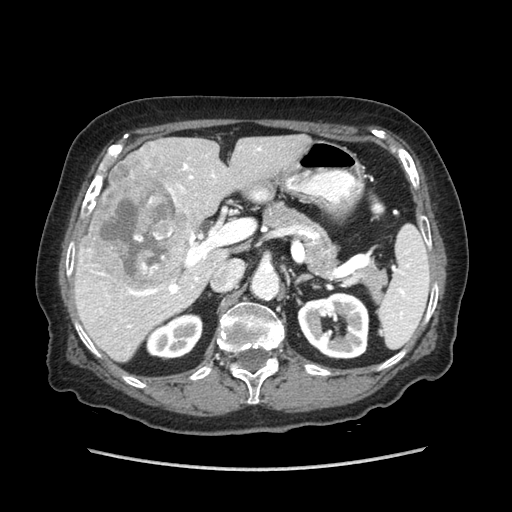
Contrast-enhanced abdominal CT (liver protocol), one axial slice. Position 43 of 89 along the scan axis. Reconstruction kernel STANDARD. Soft-tissue window (W 400 / L 40 HU). 2.5 mm slice thickness. 512 × 512 image matrix, field of view 360 × 360 mm. From the clinical record (not read from this slice): diagnosis: hepatocellular carcinoma (patient treated with transarterial chemoembolisation; whether this scan precedes or follows treatment is not stated here); TNM stage (as recorded): Stage-IIIA; Child-Pugh class: A.
Annotated regions visible in this slice (semi-automatically segmented with operator editing):
- liver parenchyma outside the tumour (the mass and vessels are separate outlines, so this box may not span the whole liver): bounding box [x1, y1, x2, y2] px = [74, 134, 310, 362]
- mass: [79, 165, 195, 295]
- liver vessels: [99, 147, 261, 328]